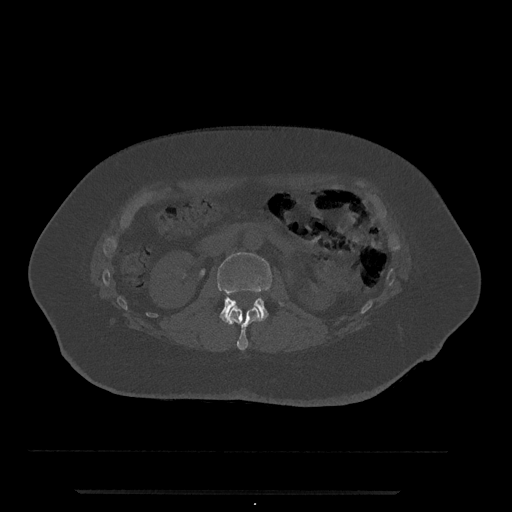
CT including the spine, one axial slice; reconstruction kernel Br40s/3; 120 kVp; bone window (W 1800 / L 400 HU); 0.5 mm slice thickness; 512 × 512 image matrix, field of view 440 × 440 mm. Patient: female, 51 years. Case-level facts recorded for this patient, not image findings: primary cancer: neuro.
Structures marked on this image (semi-automatic segmentation, software-assisted and operator-edited):
- L1 vertebra: bounding box (x1, y1, x2, y2) in pixels: (224, 307, 261, 351)
- L2 vertebra: (217, 252, 283, 323)